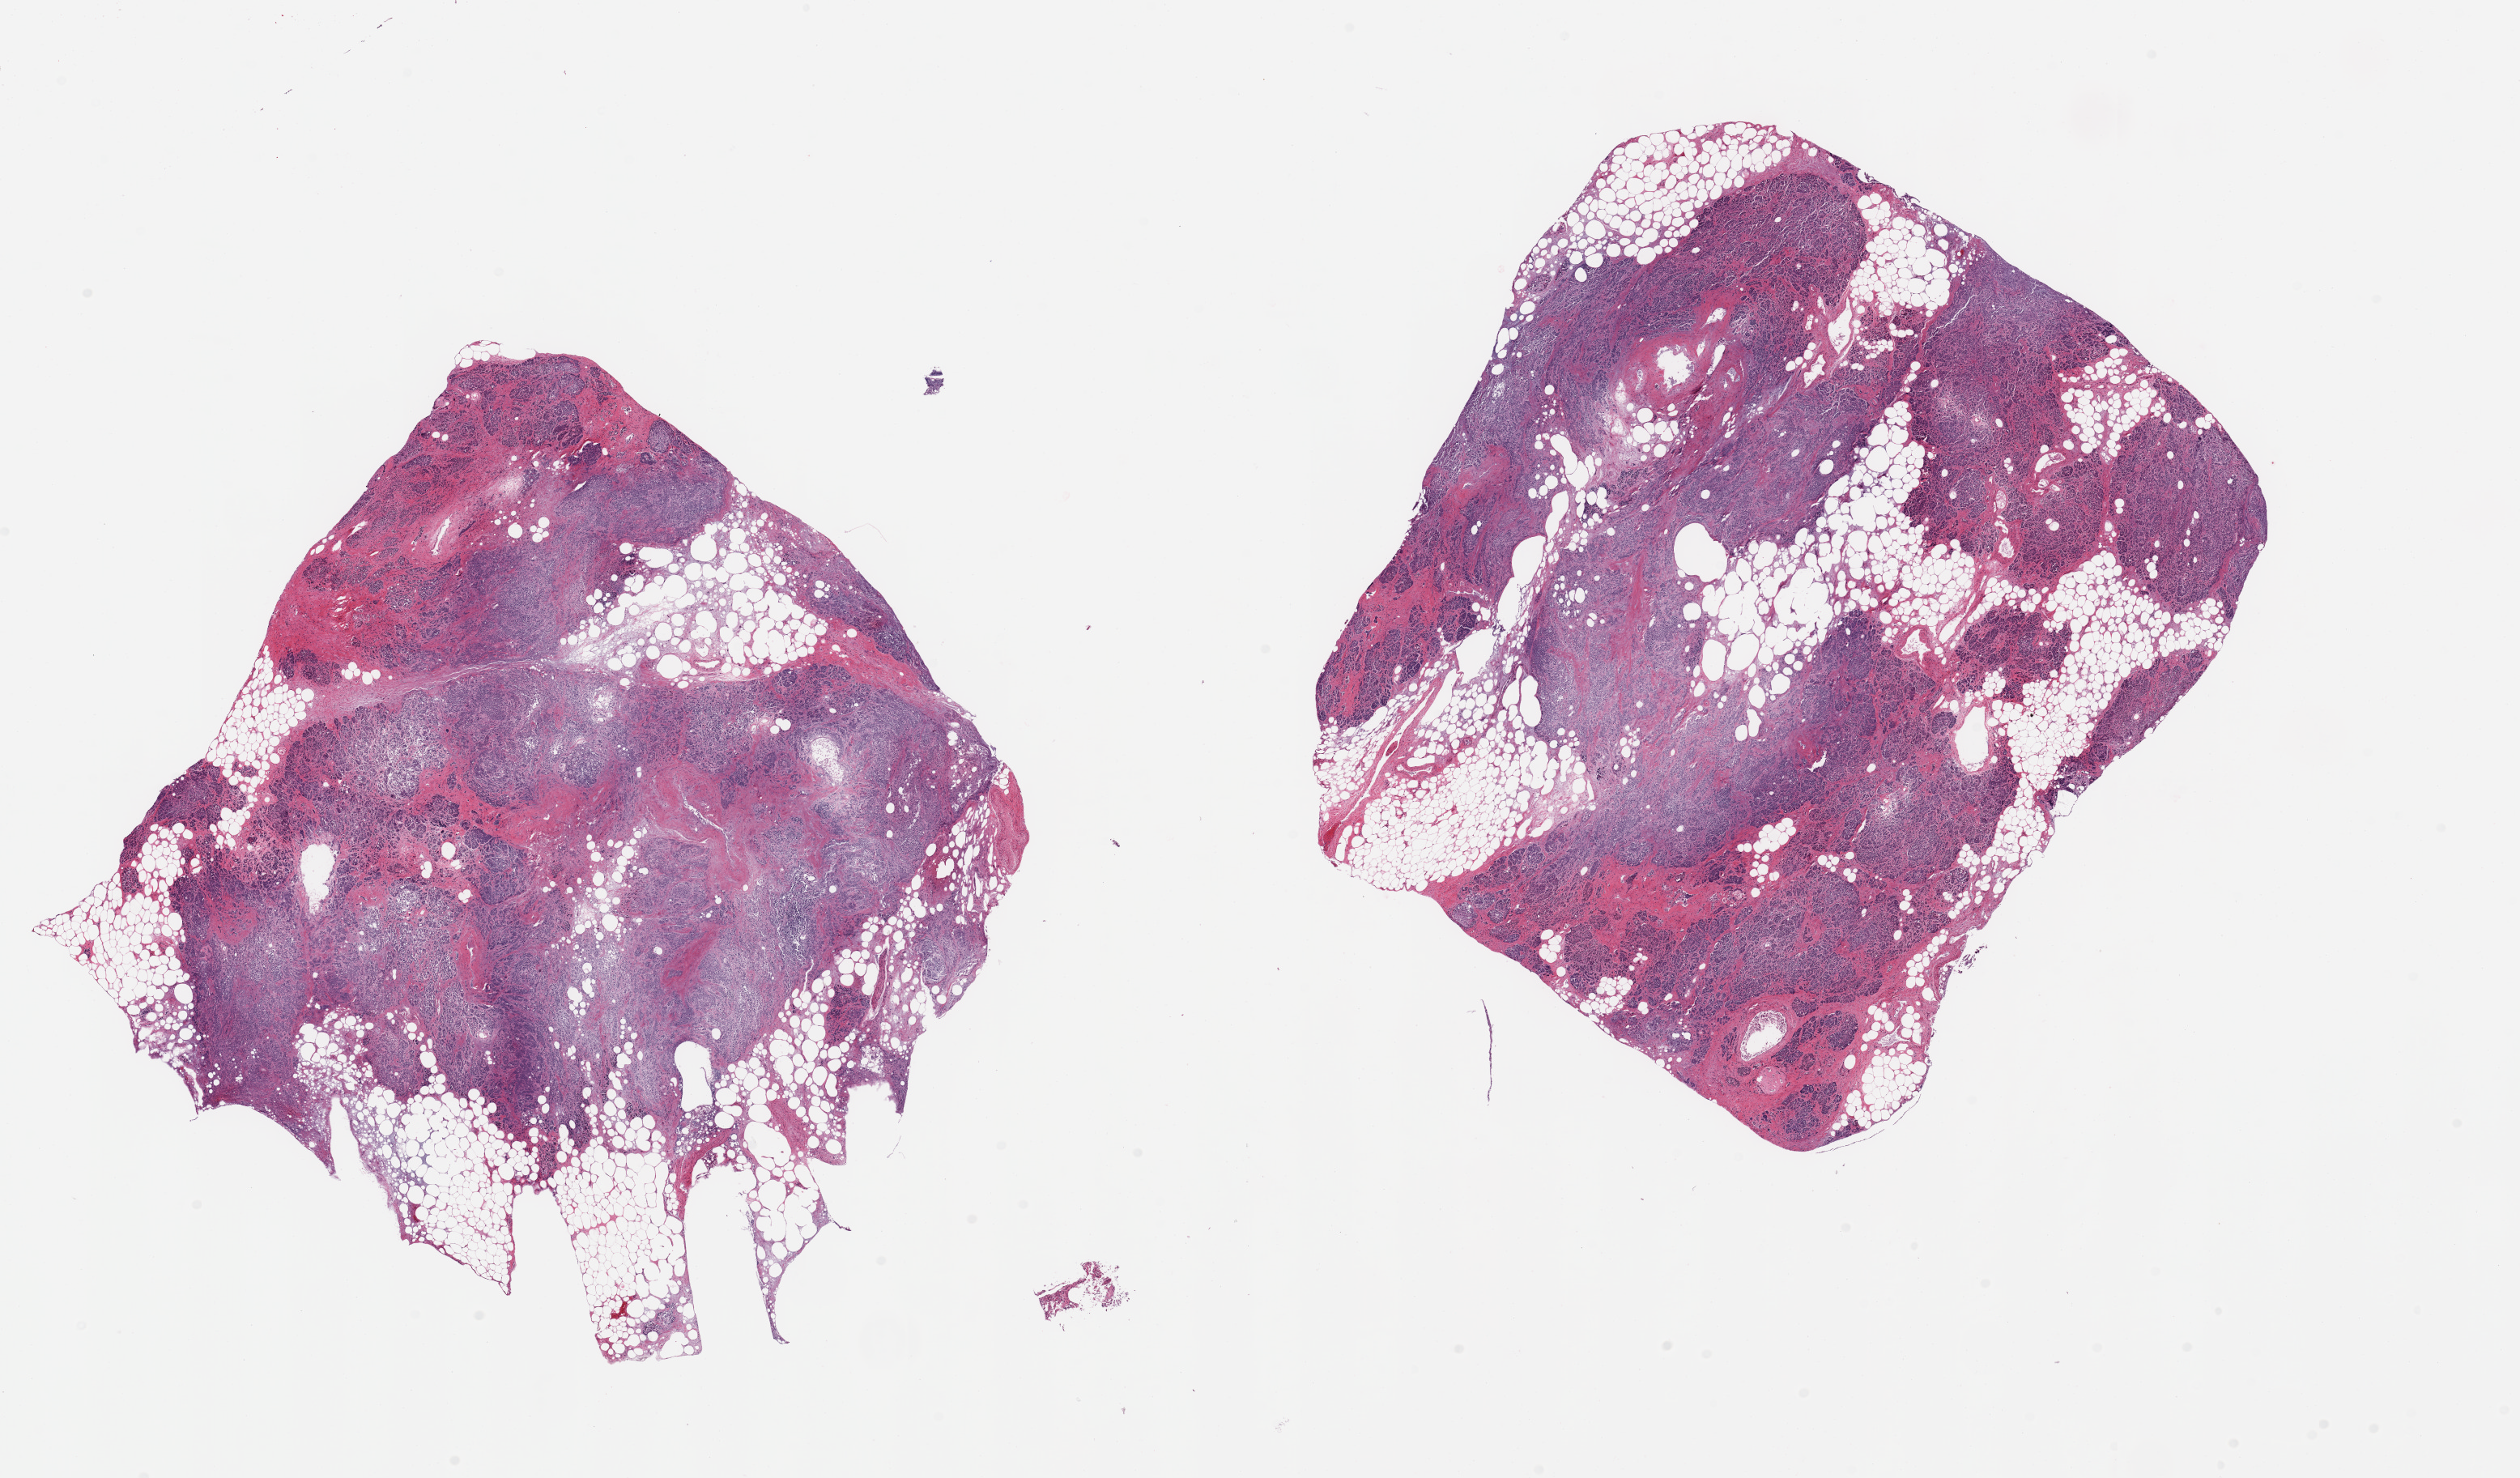
Hematoxylin and eosin (H&E) whole-slide image — shown as a low-resolution overview of the whole scanned area (about 24.6 x 14.4 mm). PAXgene-fixed, paraffin-embedded tissue. Target tissue: pancreas. Tissue donor sample. Male donor.
* pathologist's review note for this sample: 2 pieces; 50% fat internal content